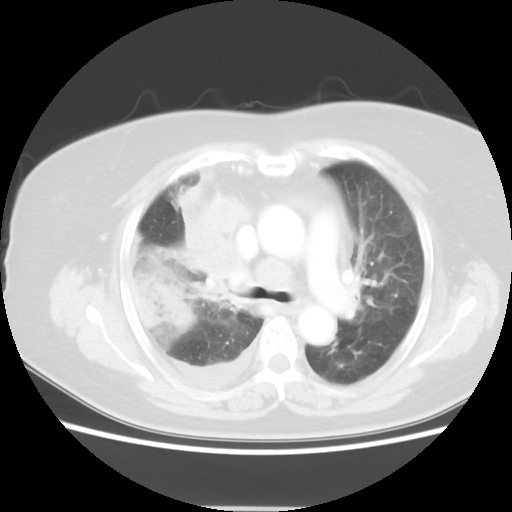
Chest CT, one axial slice; slice 32 of 48 in the series (ordered by position); reconstruction kernel STANDARD; lung window (W 1500 / L -600 HU); 5 mm slice thickness; 512 × 512 image matrix, field of view 360 × 360 mm. Female patient, age 73 years. Case-level facts recorded for this patient, not image findings: clinical TNM (as recorded): T3 N3 M1b.
Outlined on this slice (bounding box drawn by a radiologist):
- lung tumour (recorded histology: small cell carcinoma): bounding box (x1, y1, x2, y2) in pixels: (177, 189, 244, 277)